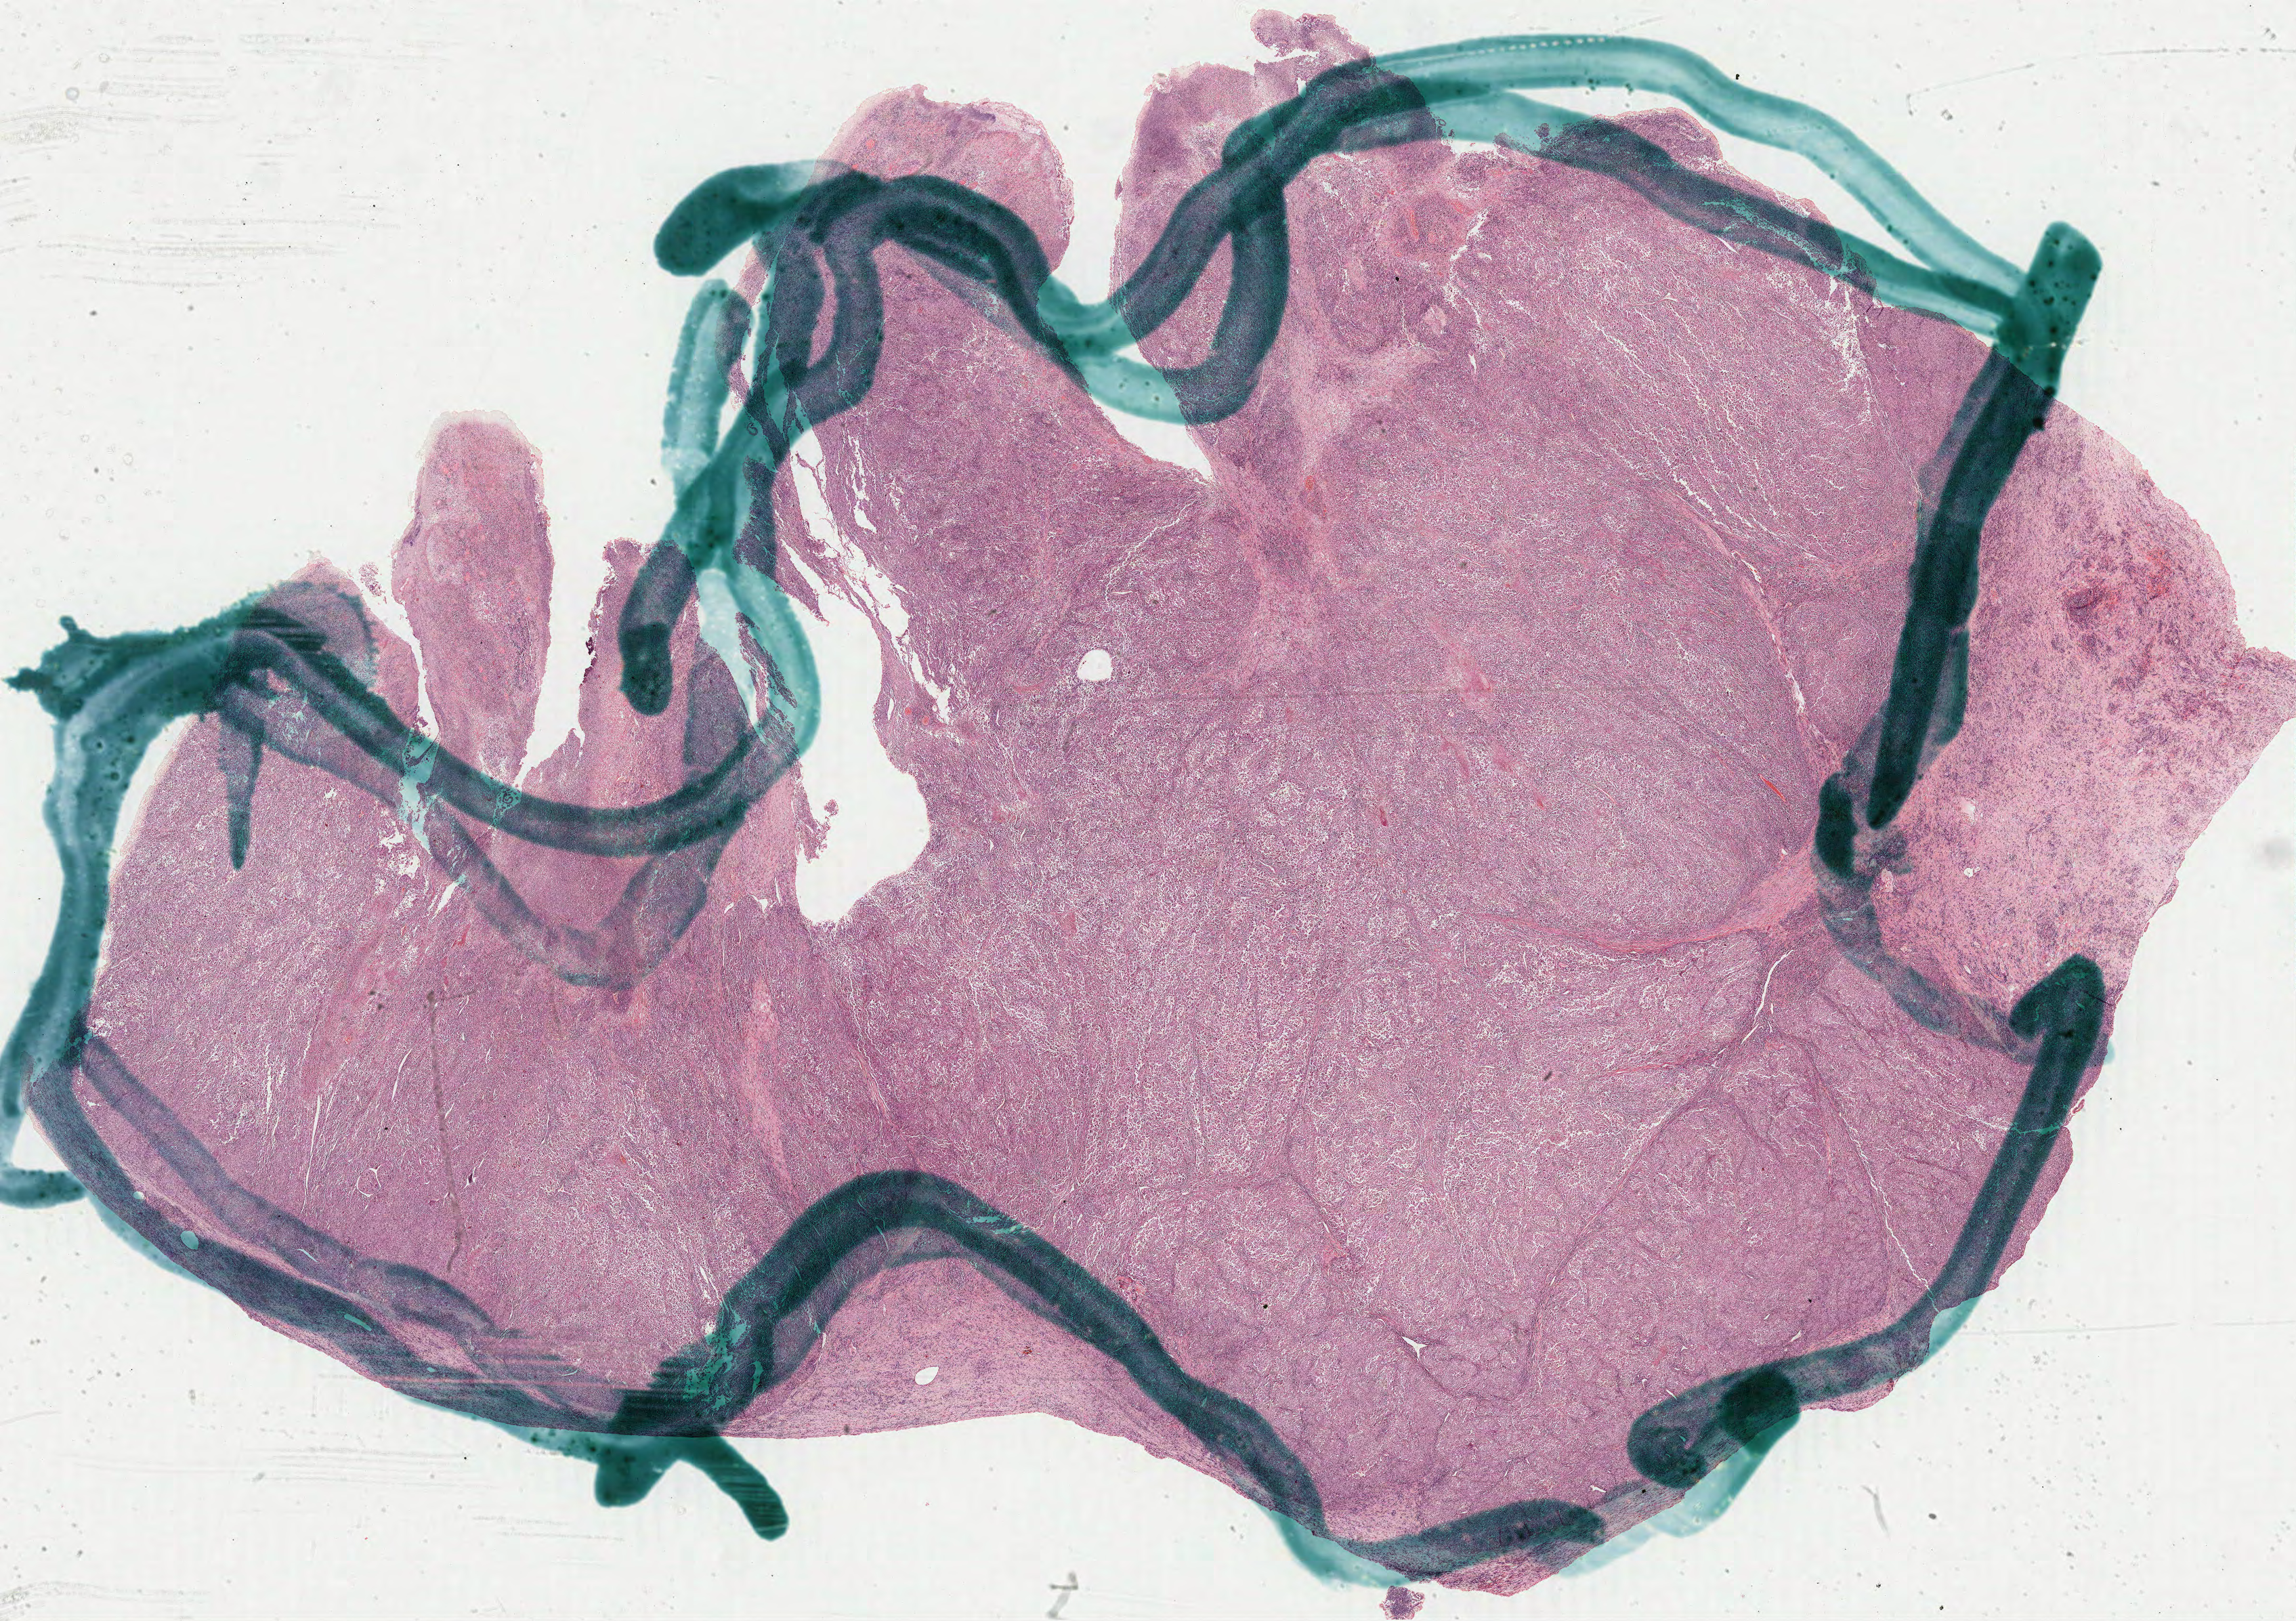
Whole-slide histology image, H&E-stained — a low-resolution overview of the entire scanned area, about 27.2 x 19.2 mm (from a 40x scan). FFPE section. Metastatic tumour sample. Male patient; age at initial diagnosis 18 years.
This section: metastatic tumour tissue. Patient diagnosis: Malignant melanoma, NOS.